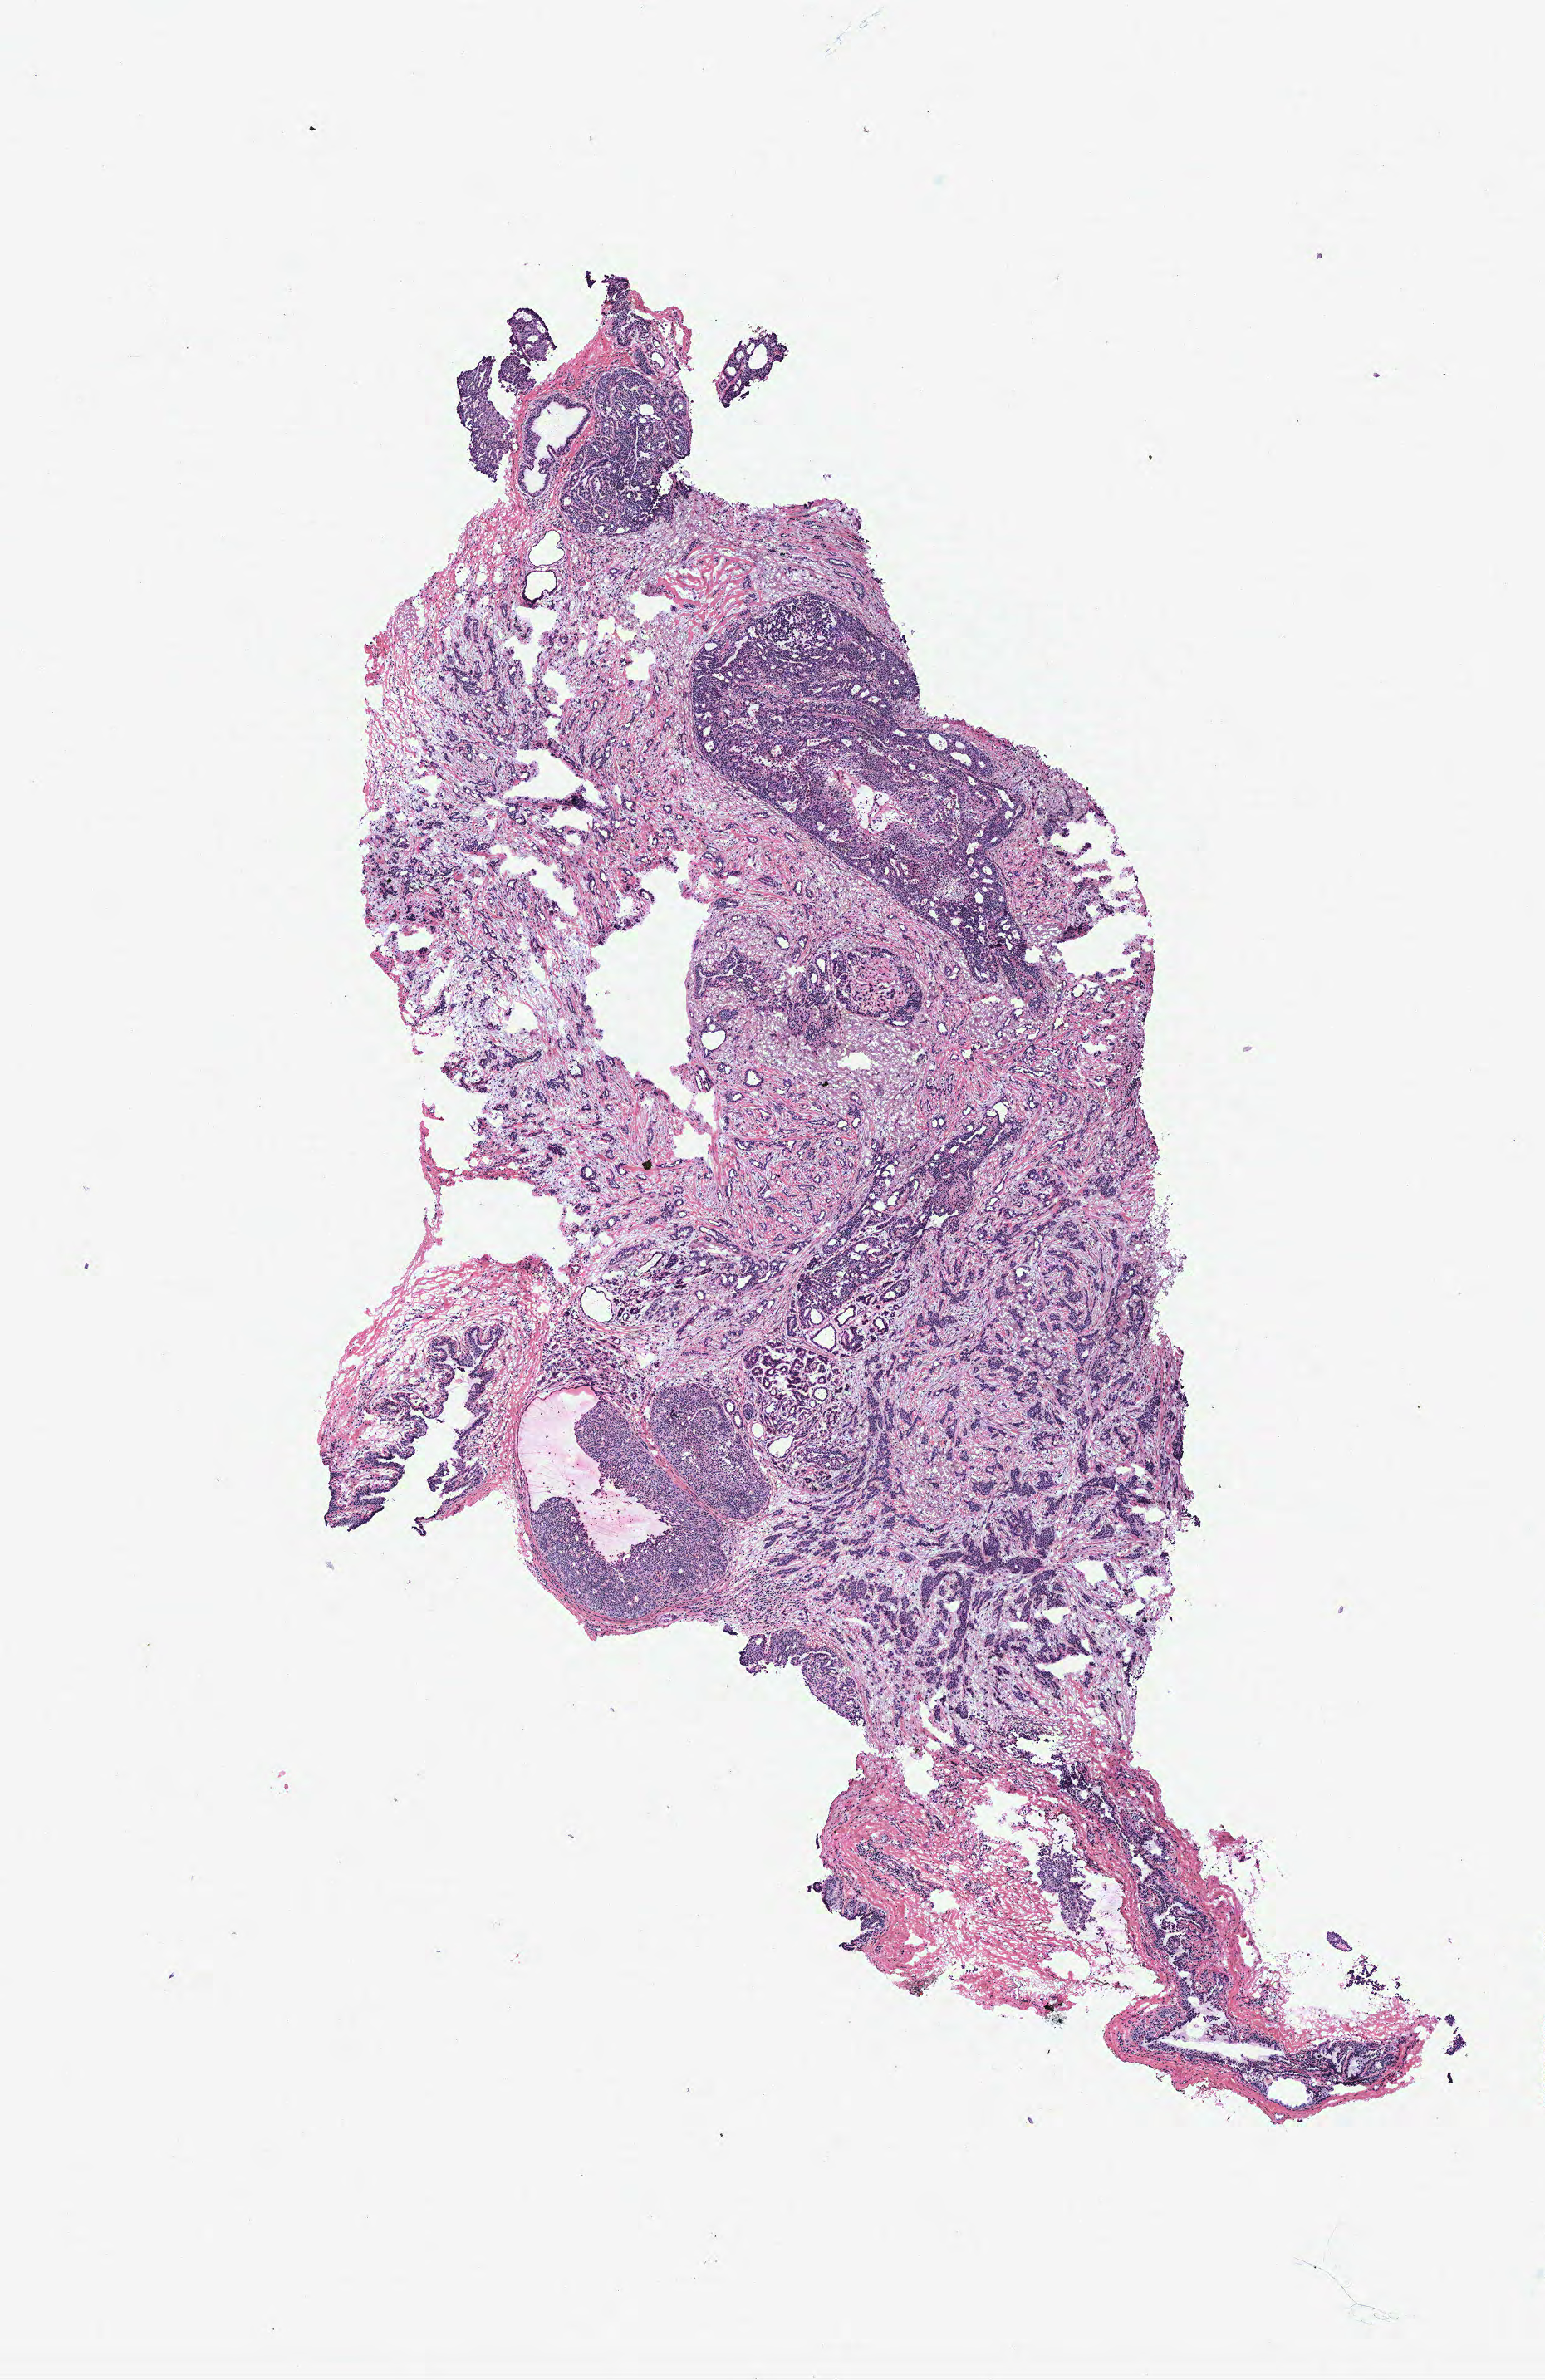
Whole-slide histology image, H&E-stained — whole scanned area (about 7.4 x 11.5 mm) shown as a low-resolution overview. Breast, tissue type not recorded. 46-year-old female patient.
• patient diagnosis: Infiltrating duct carcinoma, NOS